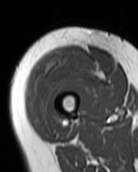
MRI of an extremity soft-tissue mass, one axial slice. Position 28 of 99 along the scan axis. MR volume resampled by the dataset authors to the PET/CT grid (not the native acquisition matrix). 3.27 mm slice thickness. 138 × 172 image matrix, field of view 135 × 168 mm. Female patient. From the clinical record (not read from this slice): histological type: pleiomorphic undifferentiated sarcoma; grade: high; site of the primary tumour: right quadricep.
Structures marked on this image (expert contour drawn on MRI and transferred to this co-registered scan by the dataset authors):
- gross tumour volume including surrounding oedema: bounding box [x1, y1, x2, y2] px = [28, 52, 104, 126]